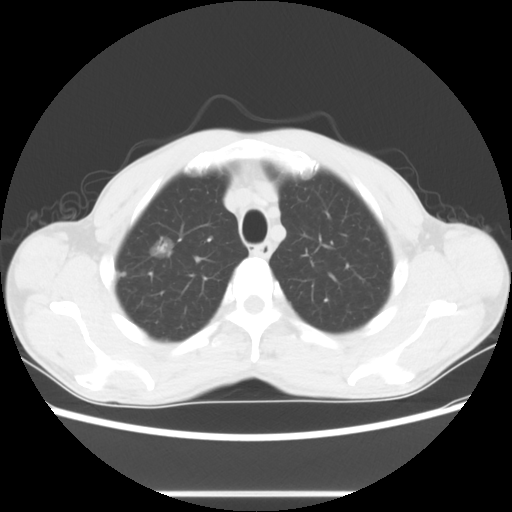
Chest CT, one axial slice; position 62 of 76 along the scan axis; reconstruction kernel STANDARD; lung window (W 1500 / L -600 HU); 5 mm slice thickness; 512 × 512 image matrix, field of view 357 × 357 mm. Male patient, age 54 years. From the clinical record (not read from this slice): clinical TNM (as recorded): T1a N0 M0.
Structures marked on this image (bounding box drawn by a radiologist):
- lung tumour (recorded histology: adenocarcinoma): bounding box [x1, y1, x2, y2] px = [144, 228, 176, 265]